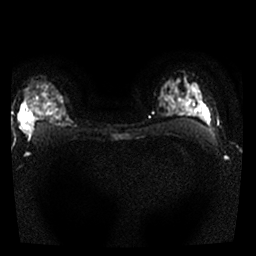
Breast MRI, one axial slice. Position 20 of 25 along the scan axis. Diffusion-weighted series; image 2 of 4 stored at this slice position (different b-values; order by instance number). 1.5 T. 4 mm slice thickness. 256 × 256 image matrix, field of view 300 × 300 mm. Female patient.
Structures marked on this image (outlined manually by an expert reader):
- tumour on diffusion-weighted imaging: bounding box (x1, y1, x2, y2) in pixels: (20, 101, 34, 135)